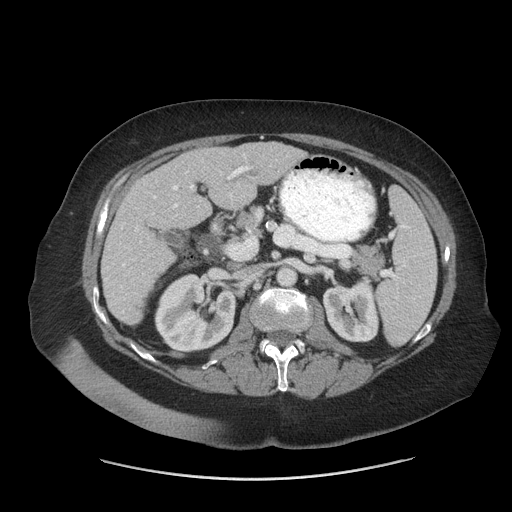
Contrast-enhanced abdominal CT (liver protocol), one axial slice. Slice 28 of 69 in the series (ordered by position). Reconstruction kernel STANDARD. Soft-tissue window (W 400 / L 40 HU). 2.5 mm slice thickness. 512 × 512 image matrix. Case-level facts recorded for this patient, not image findings: diagnosis: hepatocellular carcinoma (patient treated with transarterial chemoembolisation; whether this scan precedes or follows treatment is not stated here); TNM stage (as recorded): Stage-IIIB; Child-Pugh class: A; tumour nodularity: multinodular.
Structures marked on this image (semi-automatically segmented with operator editing):
- liver parenchyma outside the tumour (the mass and vessels are separate outlines, so this box may not span the whole liver): bounding box (x1, y1, x2, y2) in pixels: (102, 142, 306, 324)
- liver vessels: (122, 155, 249, 267)